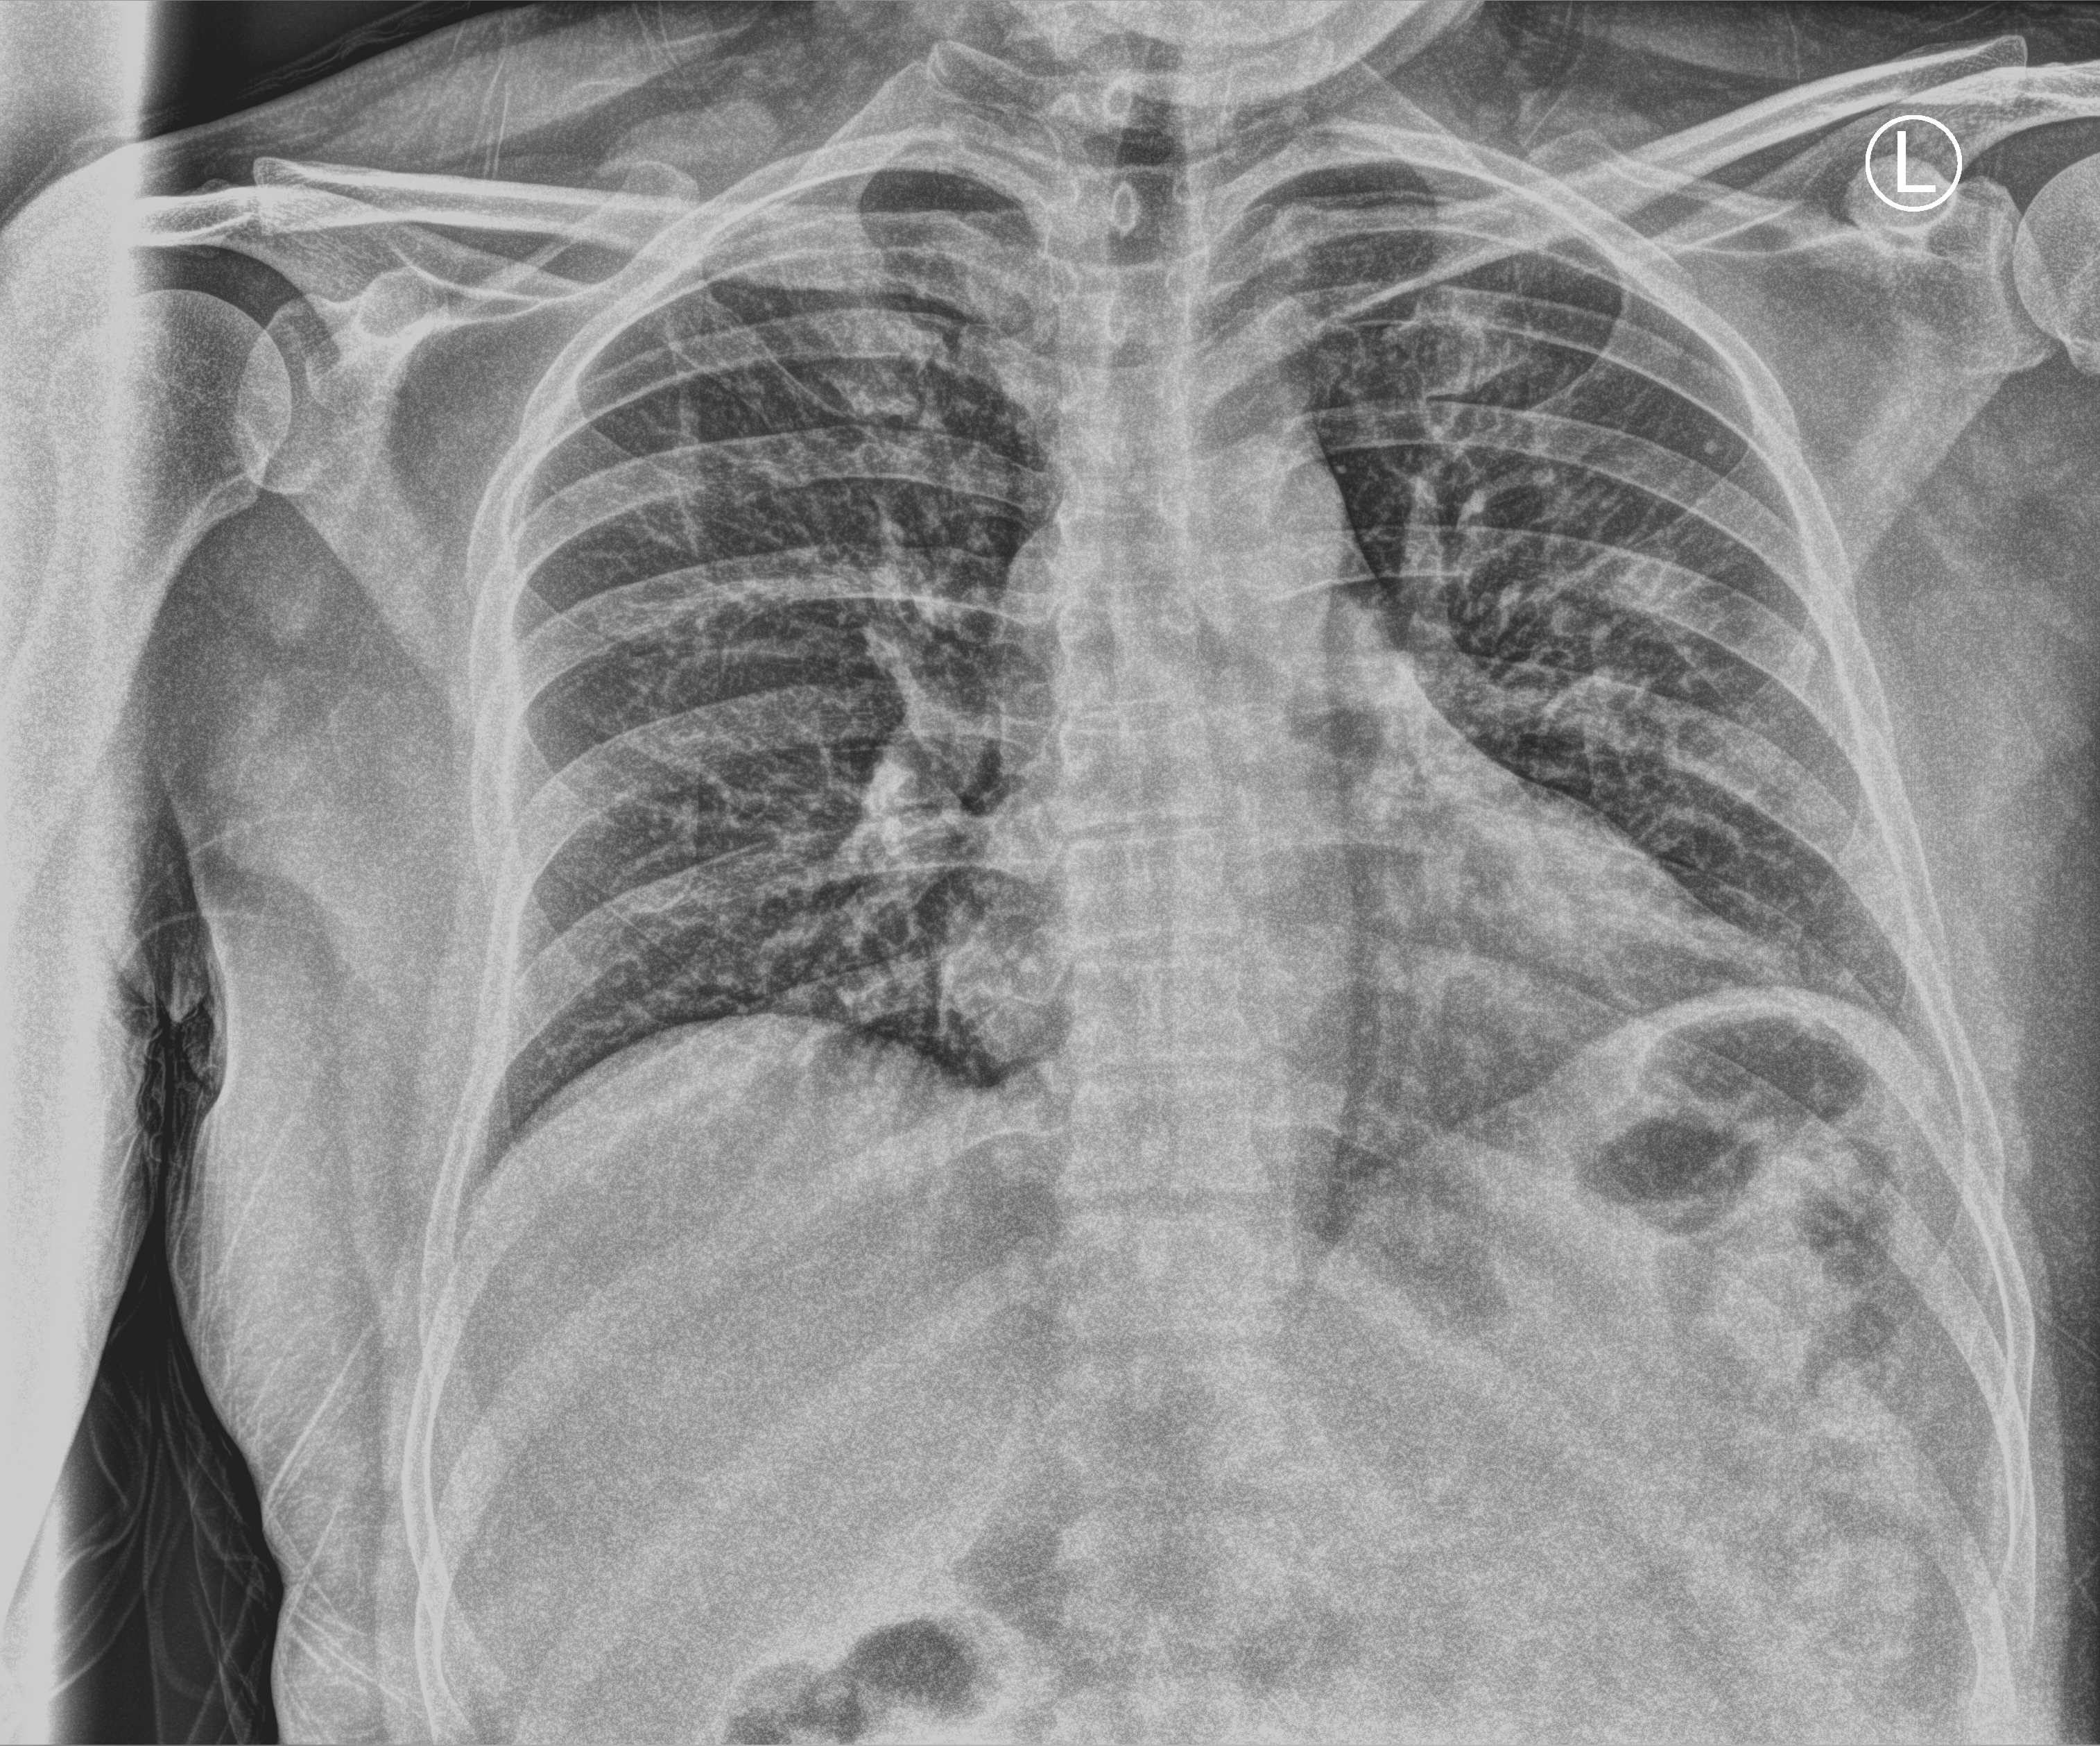
Bedside chest radiograph (computed radiography). Male patient hospitalised with COVID-19, age 18–59 years.
Hospital-stay facts (about this admission, not read from this image; timing relative to this image not recorded): mechanically ventilated during this hospital stay: no; diabetes (admission record): no.